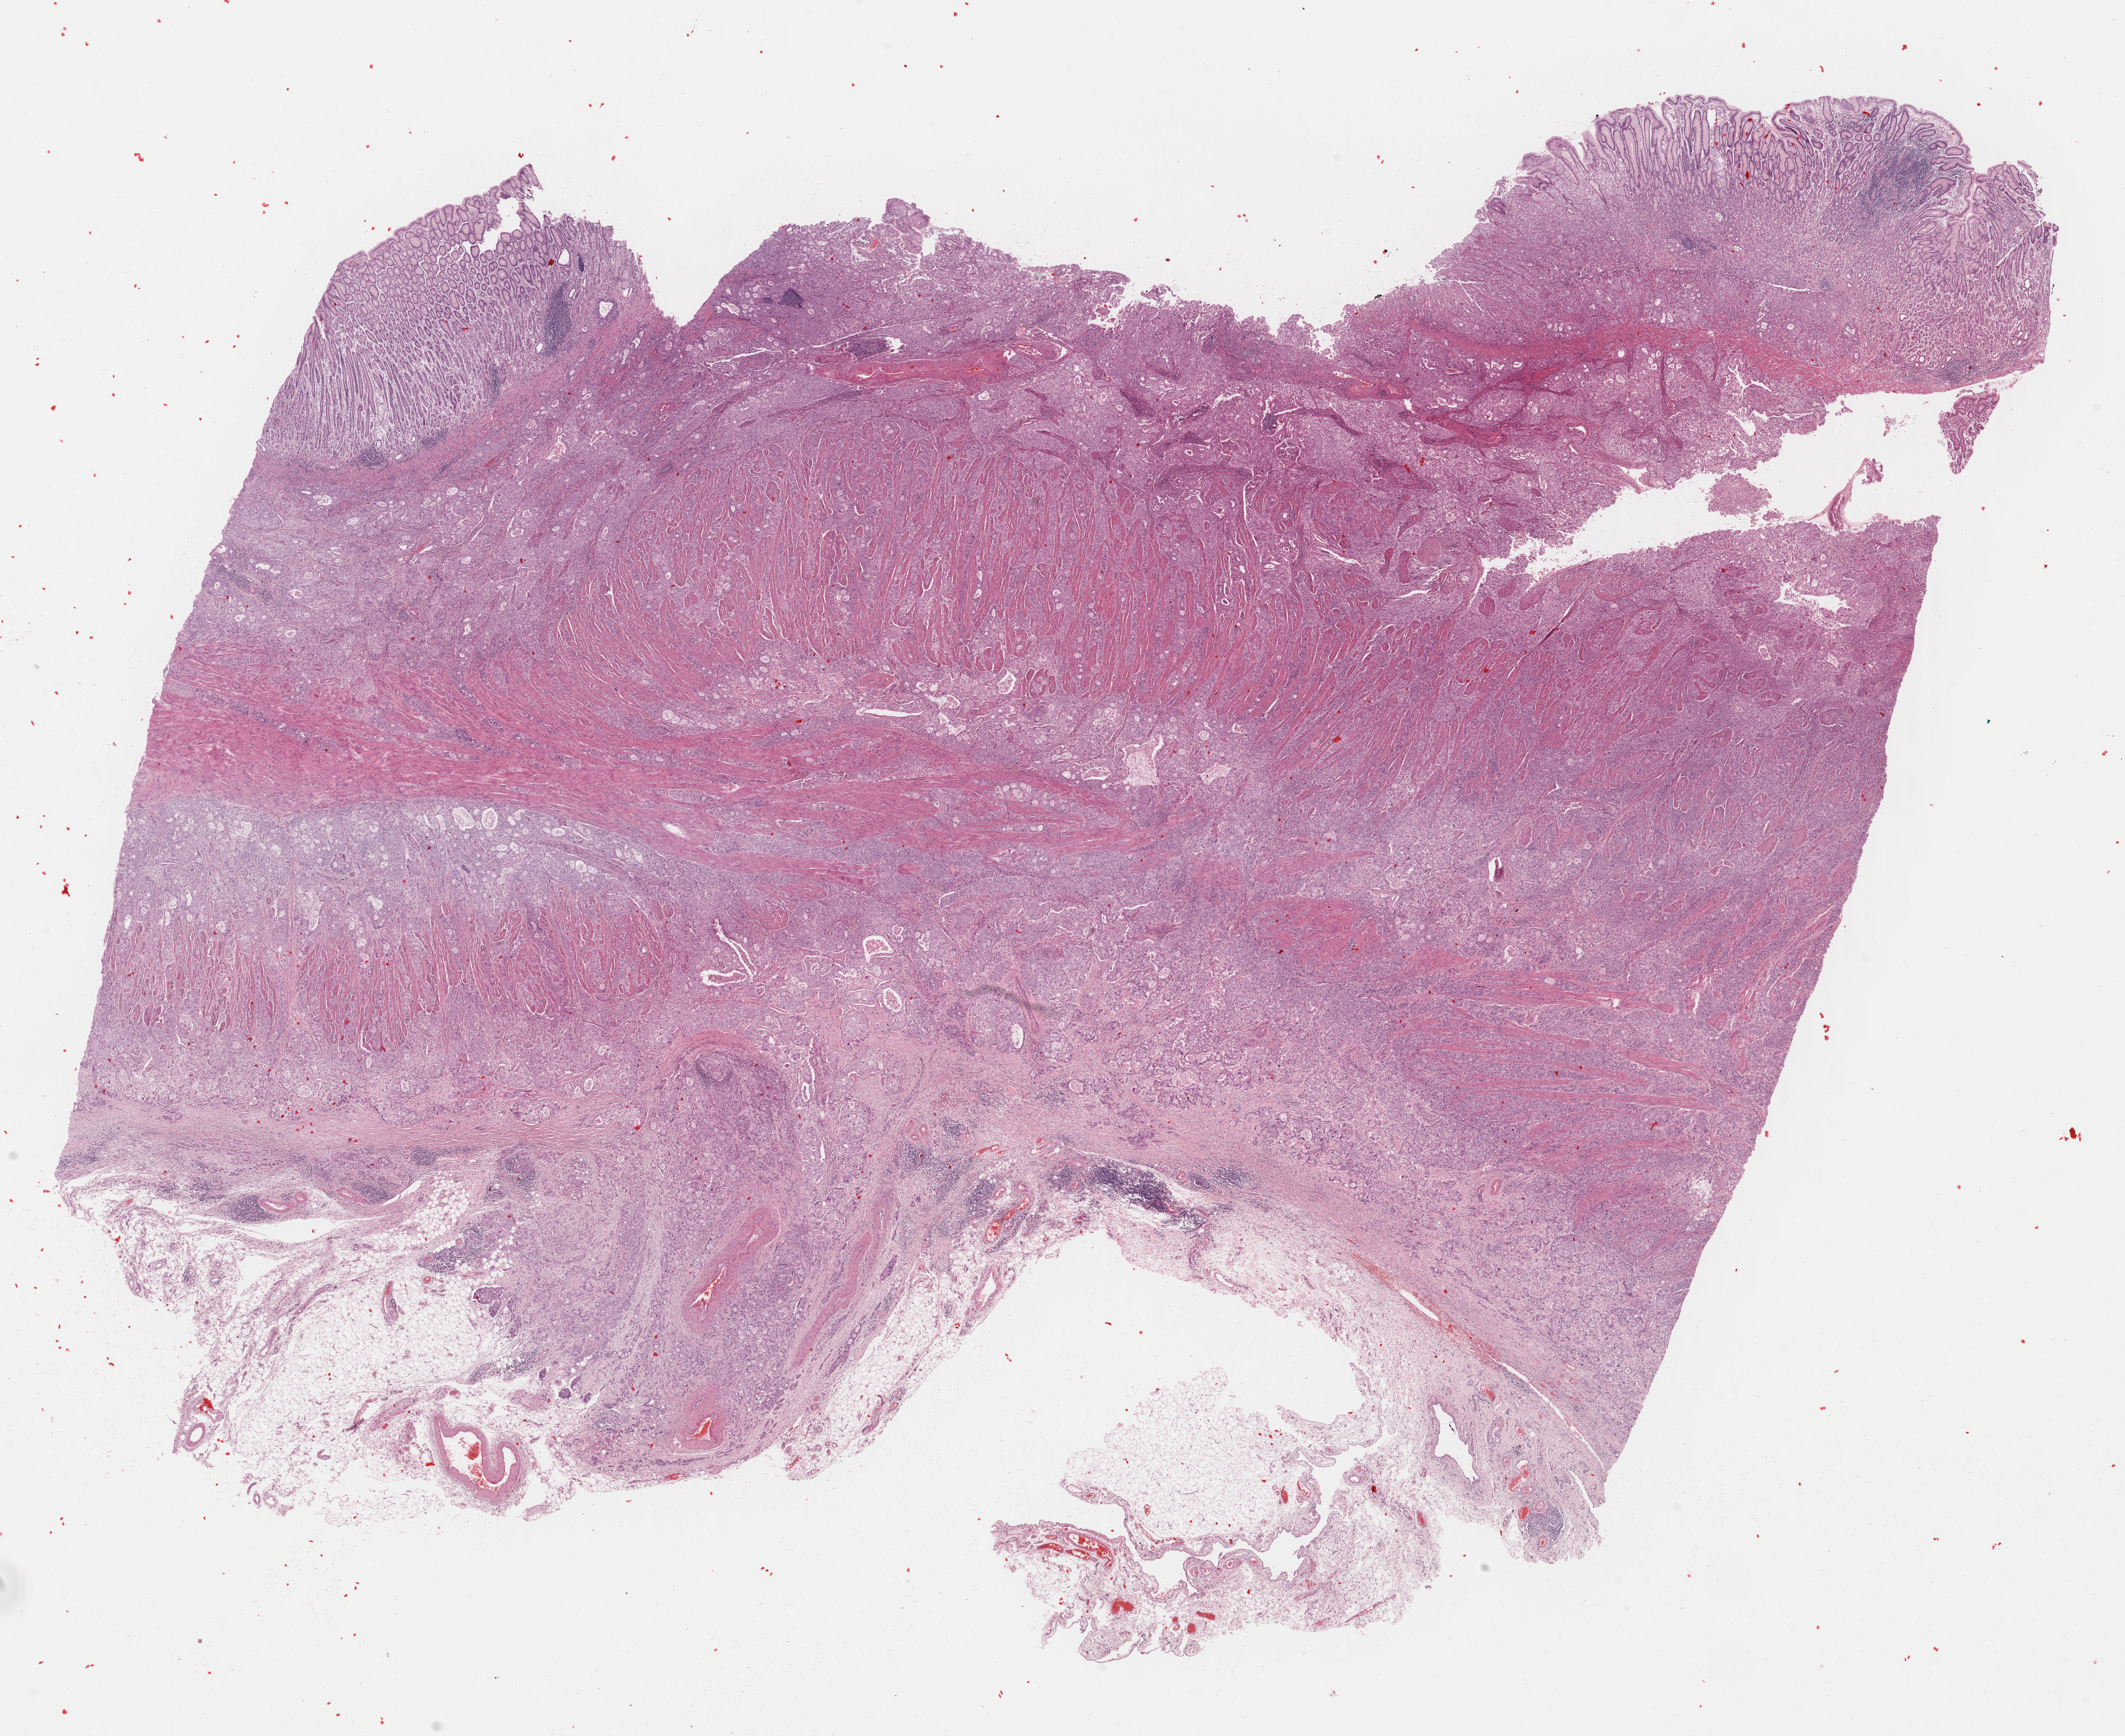
Digitized H&E tissue section (whole slide), low-resolution overview of the scanned area, about 22.9 x 18.7 mm (slide scanned at 40x); formalin-fixed paraffin-embedded (FFPE) diagnostic section; primary tumour sample from the stomach. Female, age 64 years at initial diagnosis.
Pathologic diagnosis: Carcinoma, diffuse type (cardia, NOS).